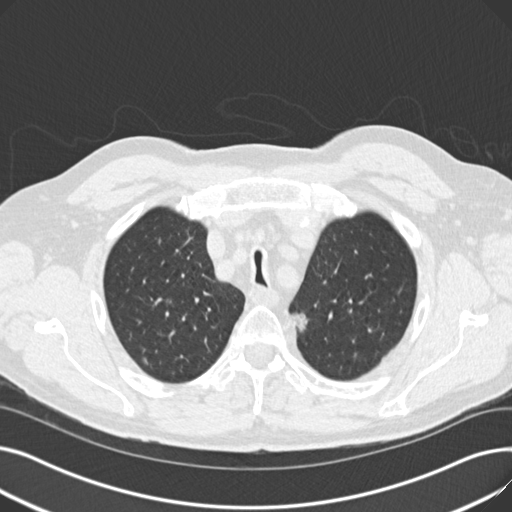
Low-dose screening chest CT, axial slice, second annual screen, lung window (W 1500 / L -600 HU), 2 mm slice thickness, slice 41 of 187 in the series, 512 × 512 image matrix, field of view 370 × 370 mm. Male, age 70 years at enrolment. Current smoker at enrolment.
• Expert reader's lesion annotation, bounding box (x1, y1, x2, y2) in pixels: (280, 301, 319, 342).
• The screening reader recorded 2 non-calcified nodules or masses ≥4 mm on this exam; which of them this box marks is not recorded.
• Lung cancer was diagnosed 581 days after this screen: mixed cell adenocarcinoma, left upper lobe, poorly differentiated (G3), stage IIB (AJCC 6th edition), 17 mm at pathology.